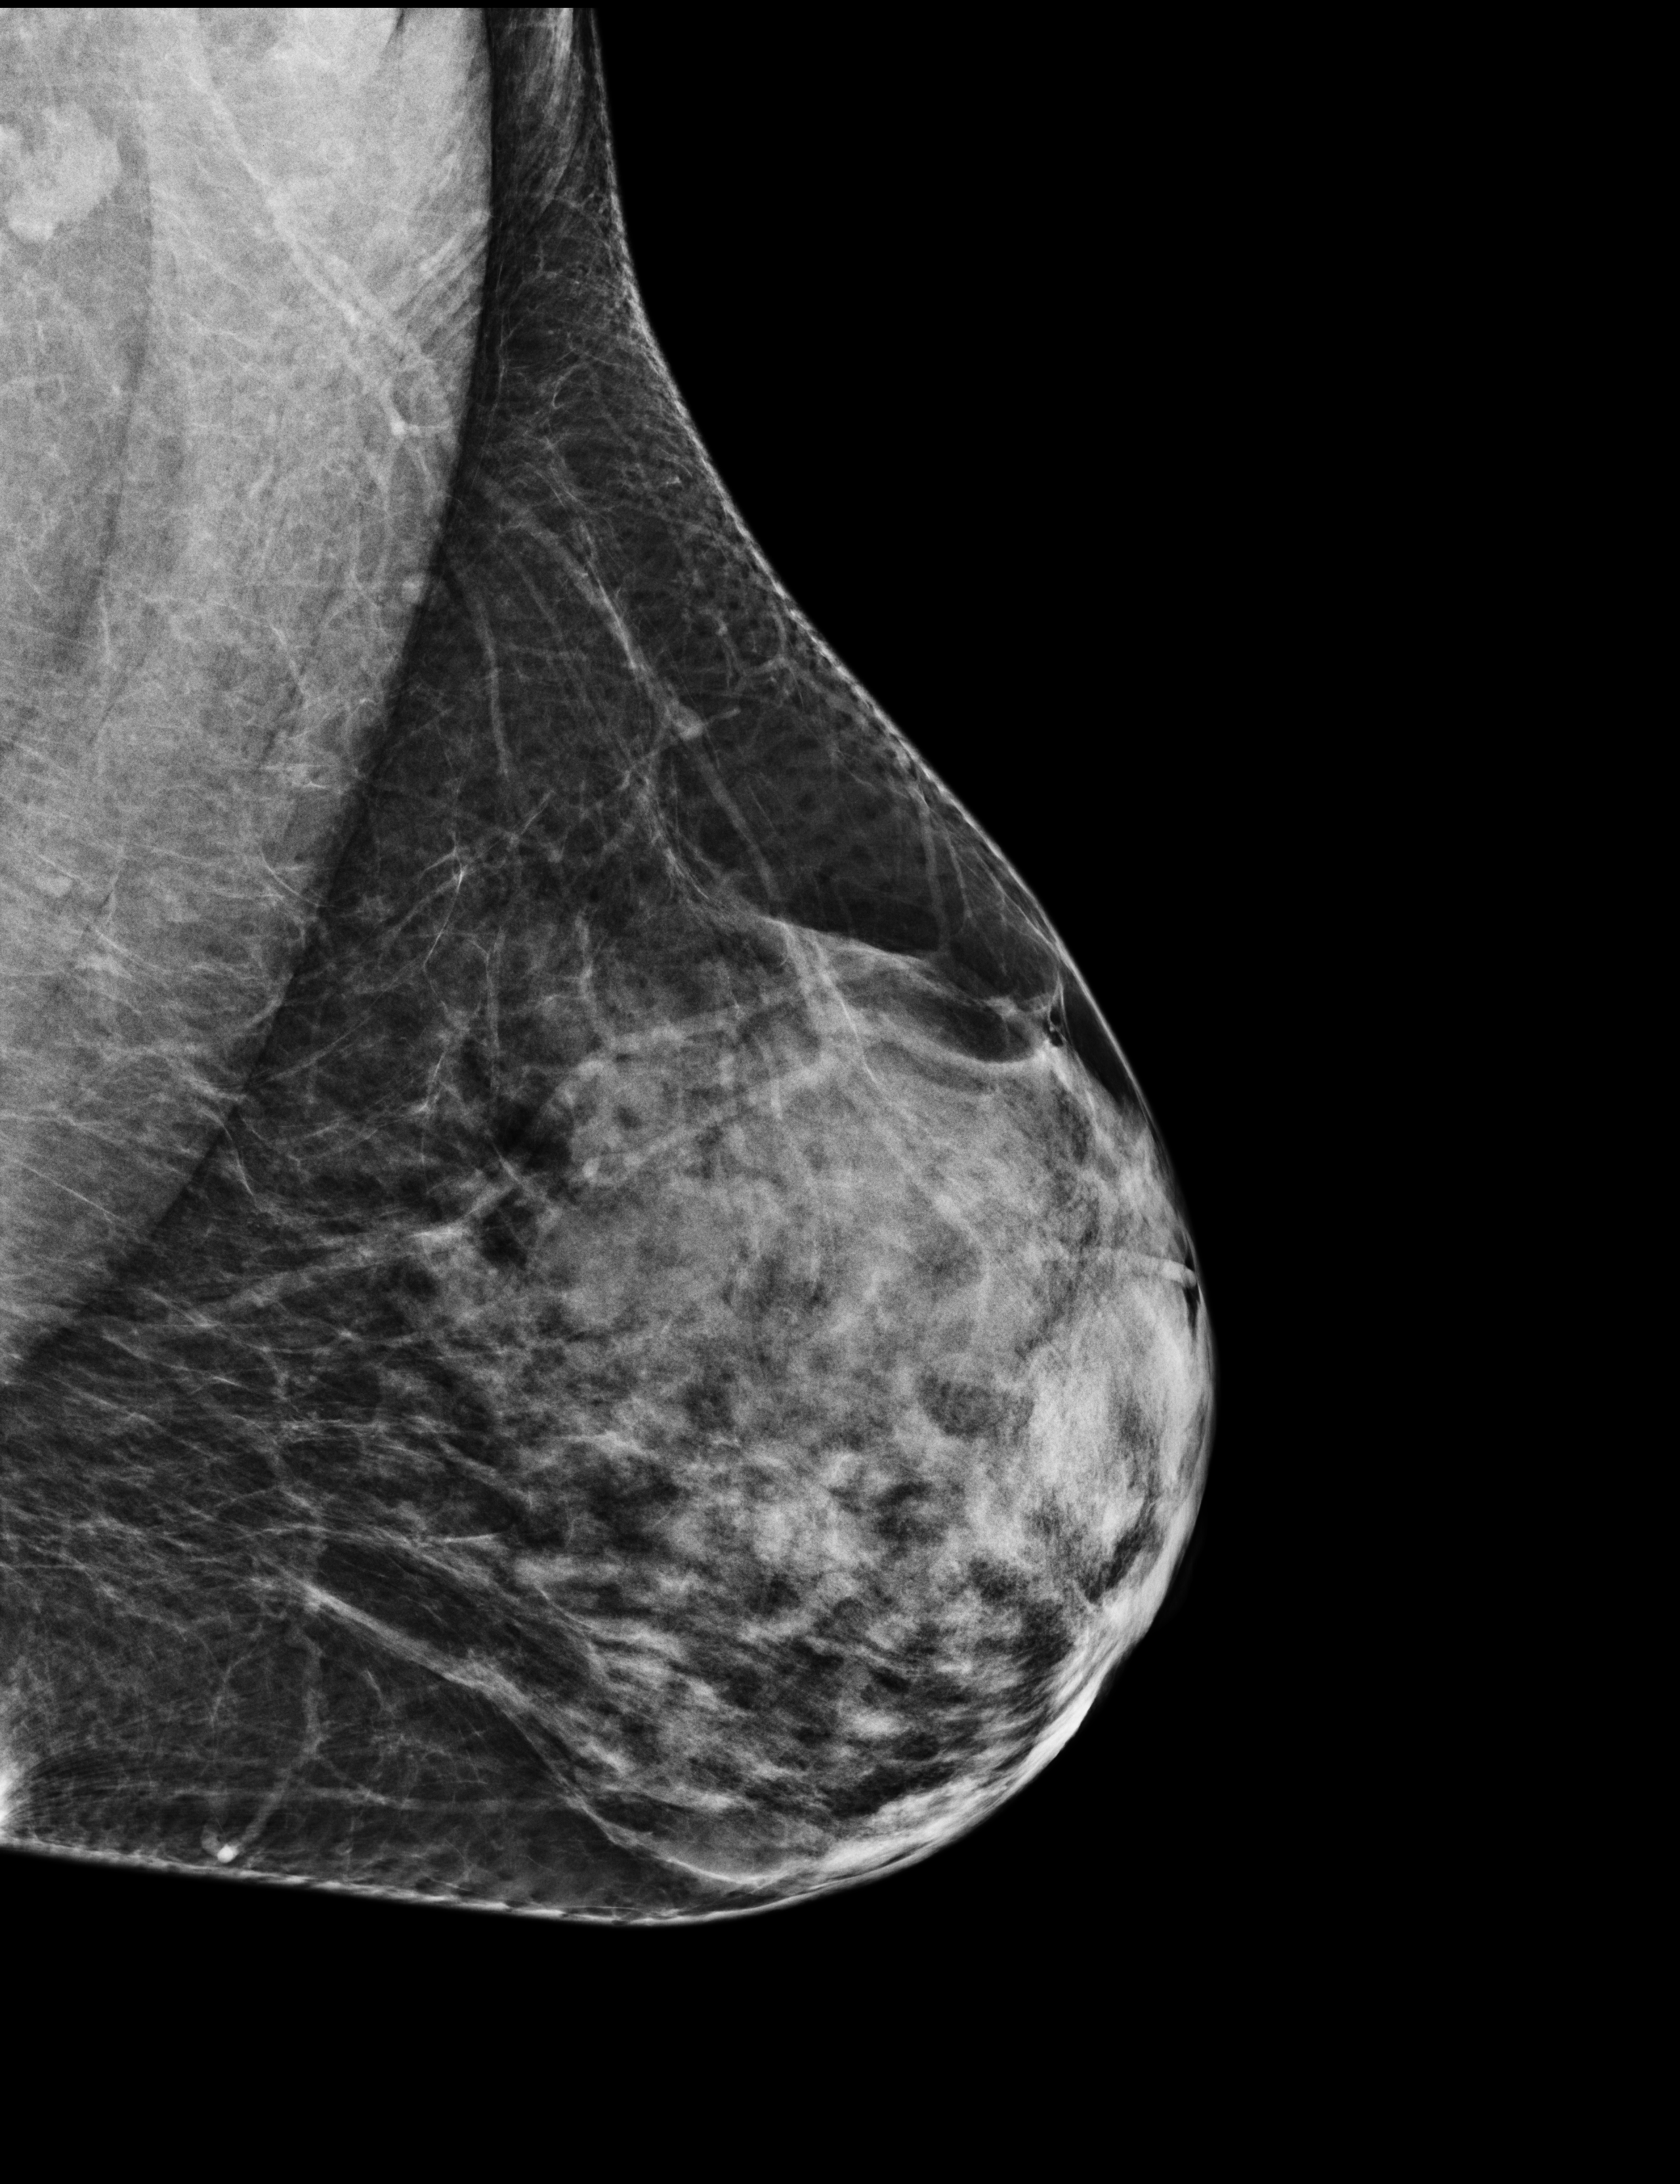
Annual screening mammography examination; compressed breast thickness 60 mm. Patient: female, 54 years.
Image type: full-field digital mammogram. Breast: left. Projection: medio-lateral oblique projection. BI-RADS breast density category at the screening exam (both breasts, scale 1–4): 3. Final BI-RADS assessment for this screening round (tomosynthesis exam, both breasts): category 1. Recall: no recall after this screen.